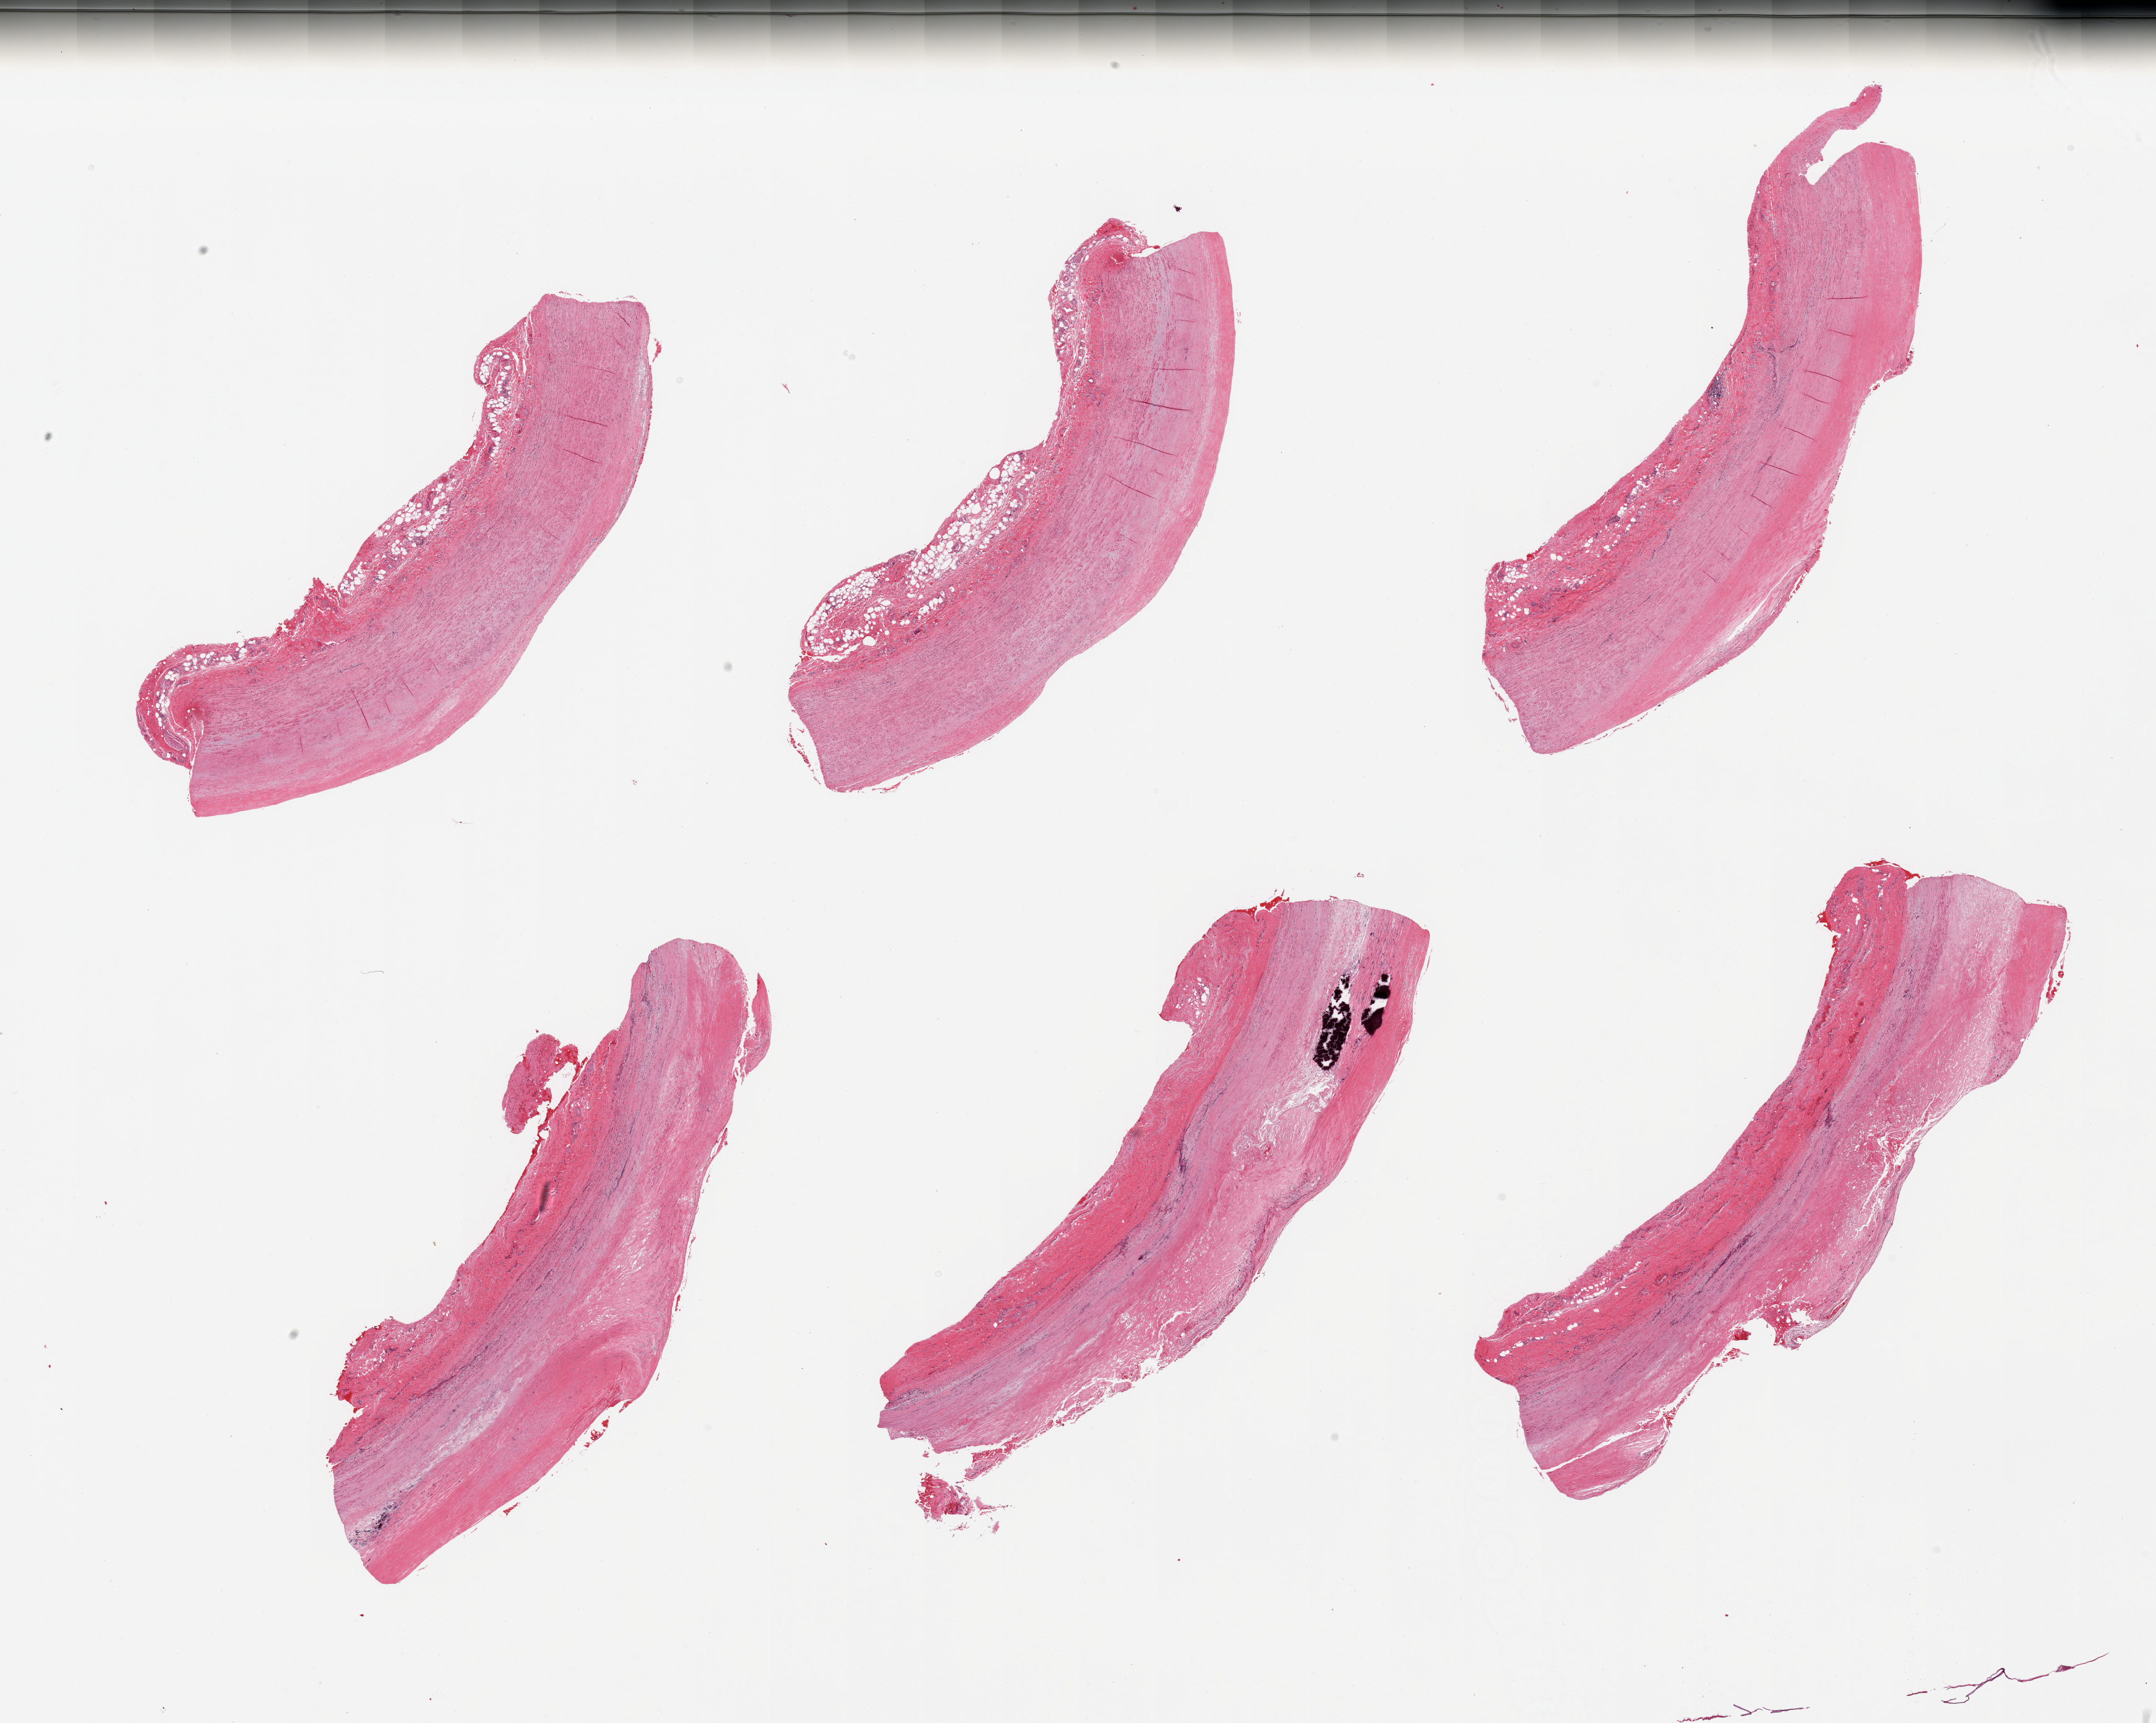
Haematoxylin and eosin whole-slide image — whole scanned area (about 27.6 x 22.0 mm) shown as a low-resolution overview. PAXgene-fixed, paraffin-embedded tissue. Section of aorta (target tissue). Donor tissue sample. Donor sex: male.
Review note (as recorded): 6 pieces; moderate, focally calcified sclerotic plaques; adventitial fat up to 0.6 mm.